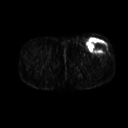
FDG PET of an extremity soft-tissue mass (from a PET/CT study), one axial slice; slice 241 of 267 in the series (ordered by position); 128 × 128 image matrix, field of view 500 × 500 mm. Male patient, age 64 years. Case-level facts recorded for this patient, not image findings: histological type: extraskeletal osteosarcoma; grade: high; site of the primary tumour: thigh.
Structures marked on this image (expert contour drawn on MRI and transferred to this co-registered scan by the dataset authors):
- gross tumour volume (mass): box from (x=87, y=39) to (x=108, y=53) px